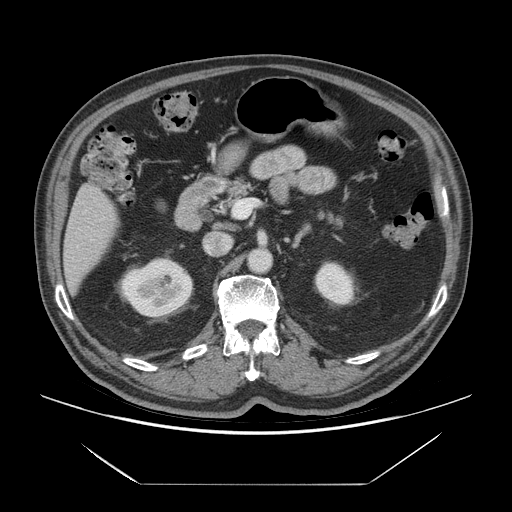
Contrast-enhanced abdominal CT (liver protocol), one axial slice; position 28 of 75 along the scan axis; soft-tissue window (W 400 / L 40 HU); 2.5 mm slice thickness; 512 × 512 image matrix, field of view 420 × 420 mm. Case-level facts recorded for this patient, not image findings: diagnosis: hepatocellular carcinoma (patient treated with transarterial chemoembolisation; whether this scan precedes or follows treatment is not stated here); TNM stage (as recorded): Stage-I; Child-Pugh class: A; tumour differentiation: well differentiated; tumour nodularity: uninodular.
Outlined on this slice (semi-automatically segmented with operator editing):
- liver parenchyma outside the tumour (the mass and vessels are separate outlines, so this box may not span the whole liver): bounding box [x1, y1, x2, y2] px = [62, 184, 116, 294]